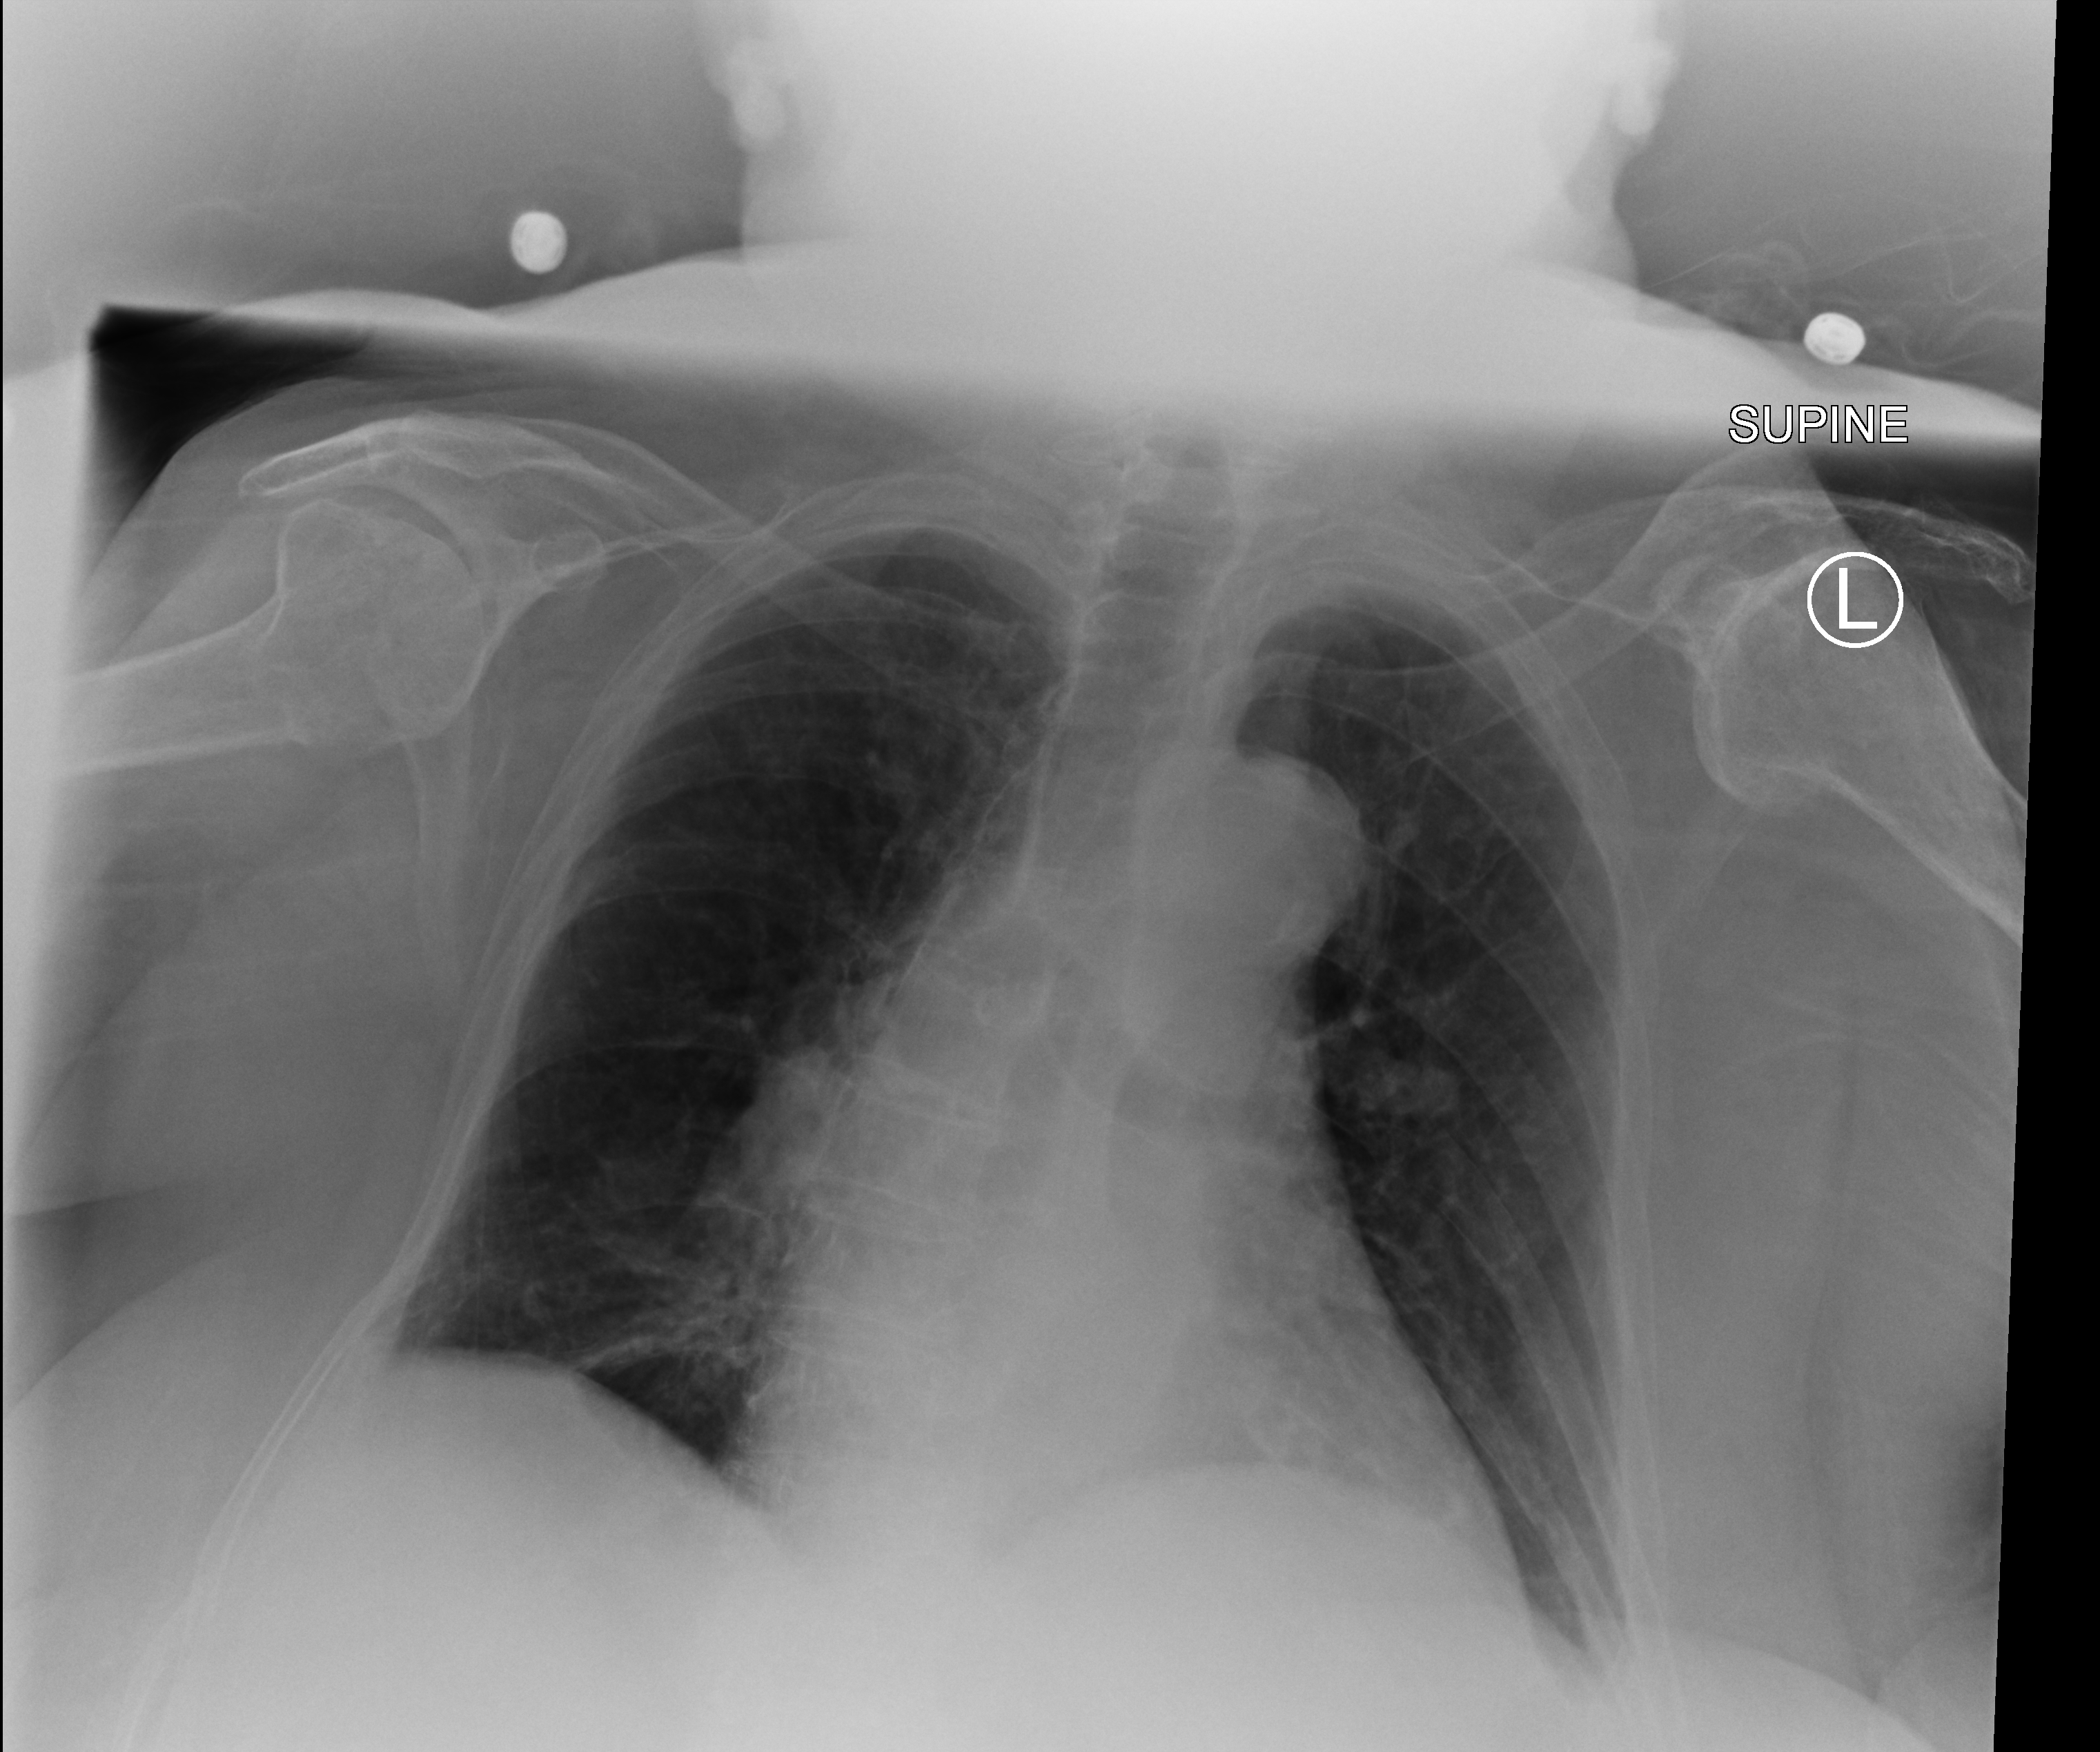
Bedside chest radiograph (computed radiography); anteroposterior (AP) projection. Patient hospitalised with COVID-19; female, aged 75–90 years.
Admission-level facts for this patient (not findings on this image; timing relative to this image not recorded):
- length of hospital stay: 12 days
- mechanically ventilated during this hospital stay: no
- admitted to intensive care during this hospital stay: yes